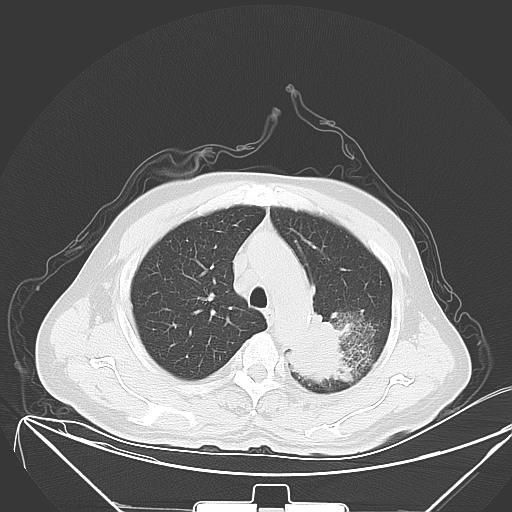
Chest CT, one axial slice; position 45 of 64 along the scan axis; lung window (W 1500 / L -600 HU); 5 mm slice thickness; 512 × 512 image matrix, field of view 431 × 431 mm. Male patient, age 58 years. Case-level facts recorded for this patient, not image findings: clinical TNM (as recorded): T2b N3 M1b; histopathological grade: G3.
Structures marked on this image (bounding box drawn by a radiologist):
- lung tumour (recorded histology: adenocarcinoma): bounding box (x1, y1, x2, y2) in pixels: (282, 307, 355, 388)